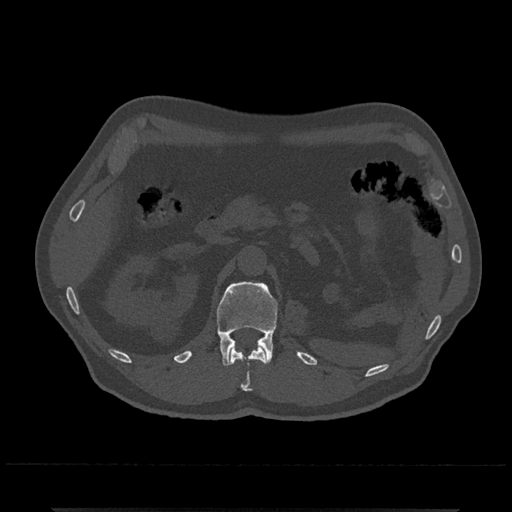
CT including the spine, one axial slice. Position 383 of 797 along the scan axis. 120 kVp. Bone window (W 1800 / L 400 HU). 0.5 mm slice thickness. 512 × 512 image matrix. Male patient, age 67 years. Case-level facts recorded for this patient, not image findings: primary cancer: prostate.
Outlined on this slice (semi-automatically segmented with operator editing):
- L1 vertebra: bounding box (x1, y1, x2, y2) in pixels: (217, 282, 278, 366)
- T12 vertebra: (230, 346, 267, 391)